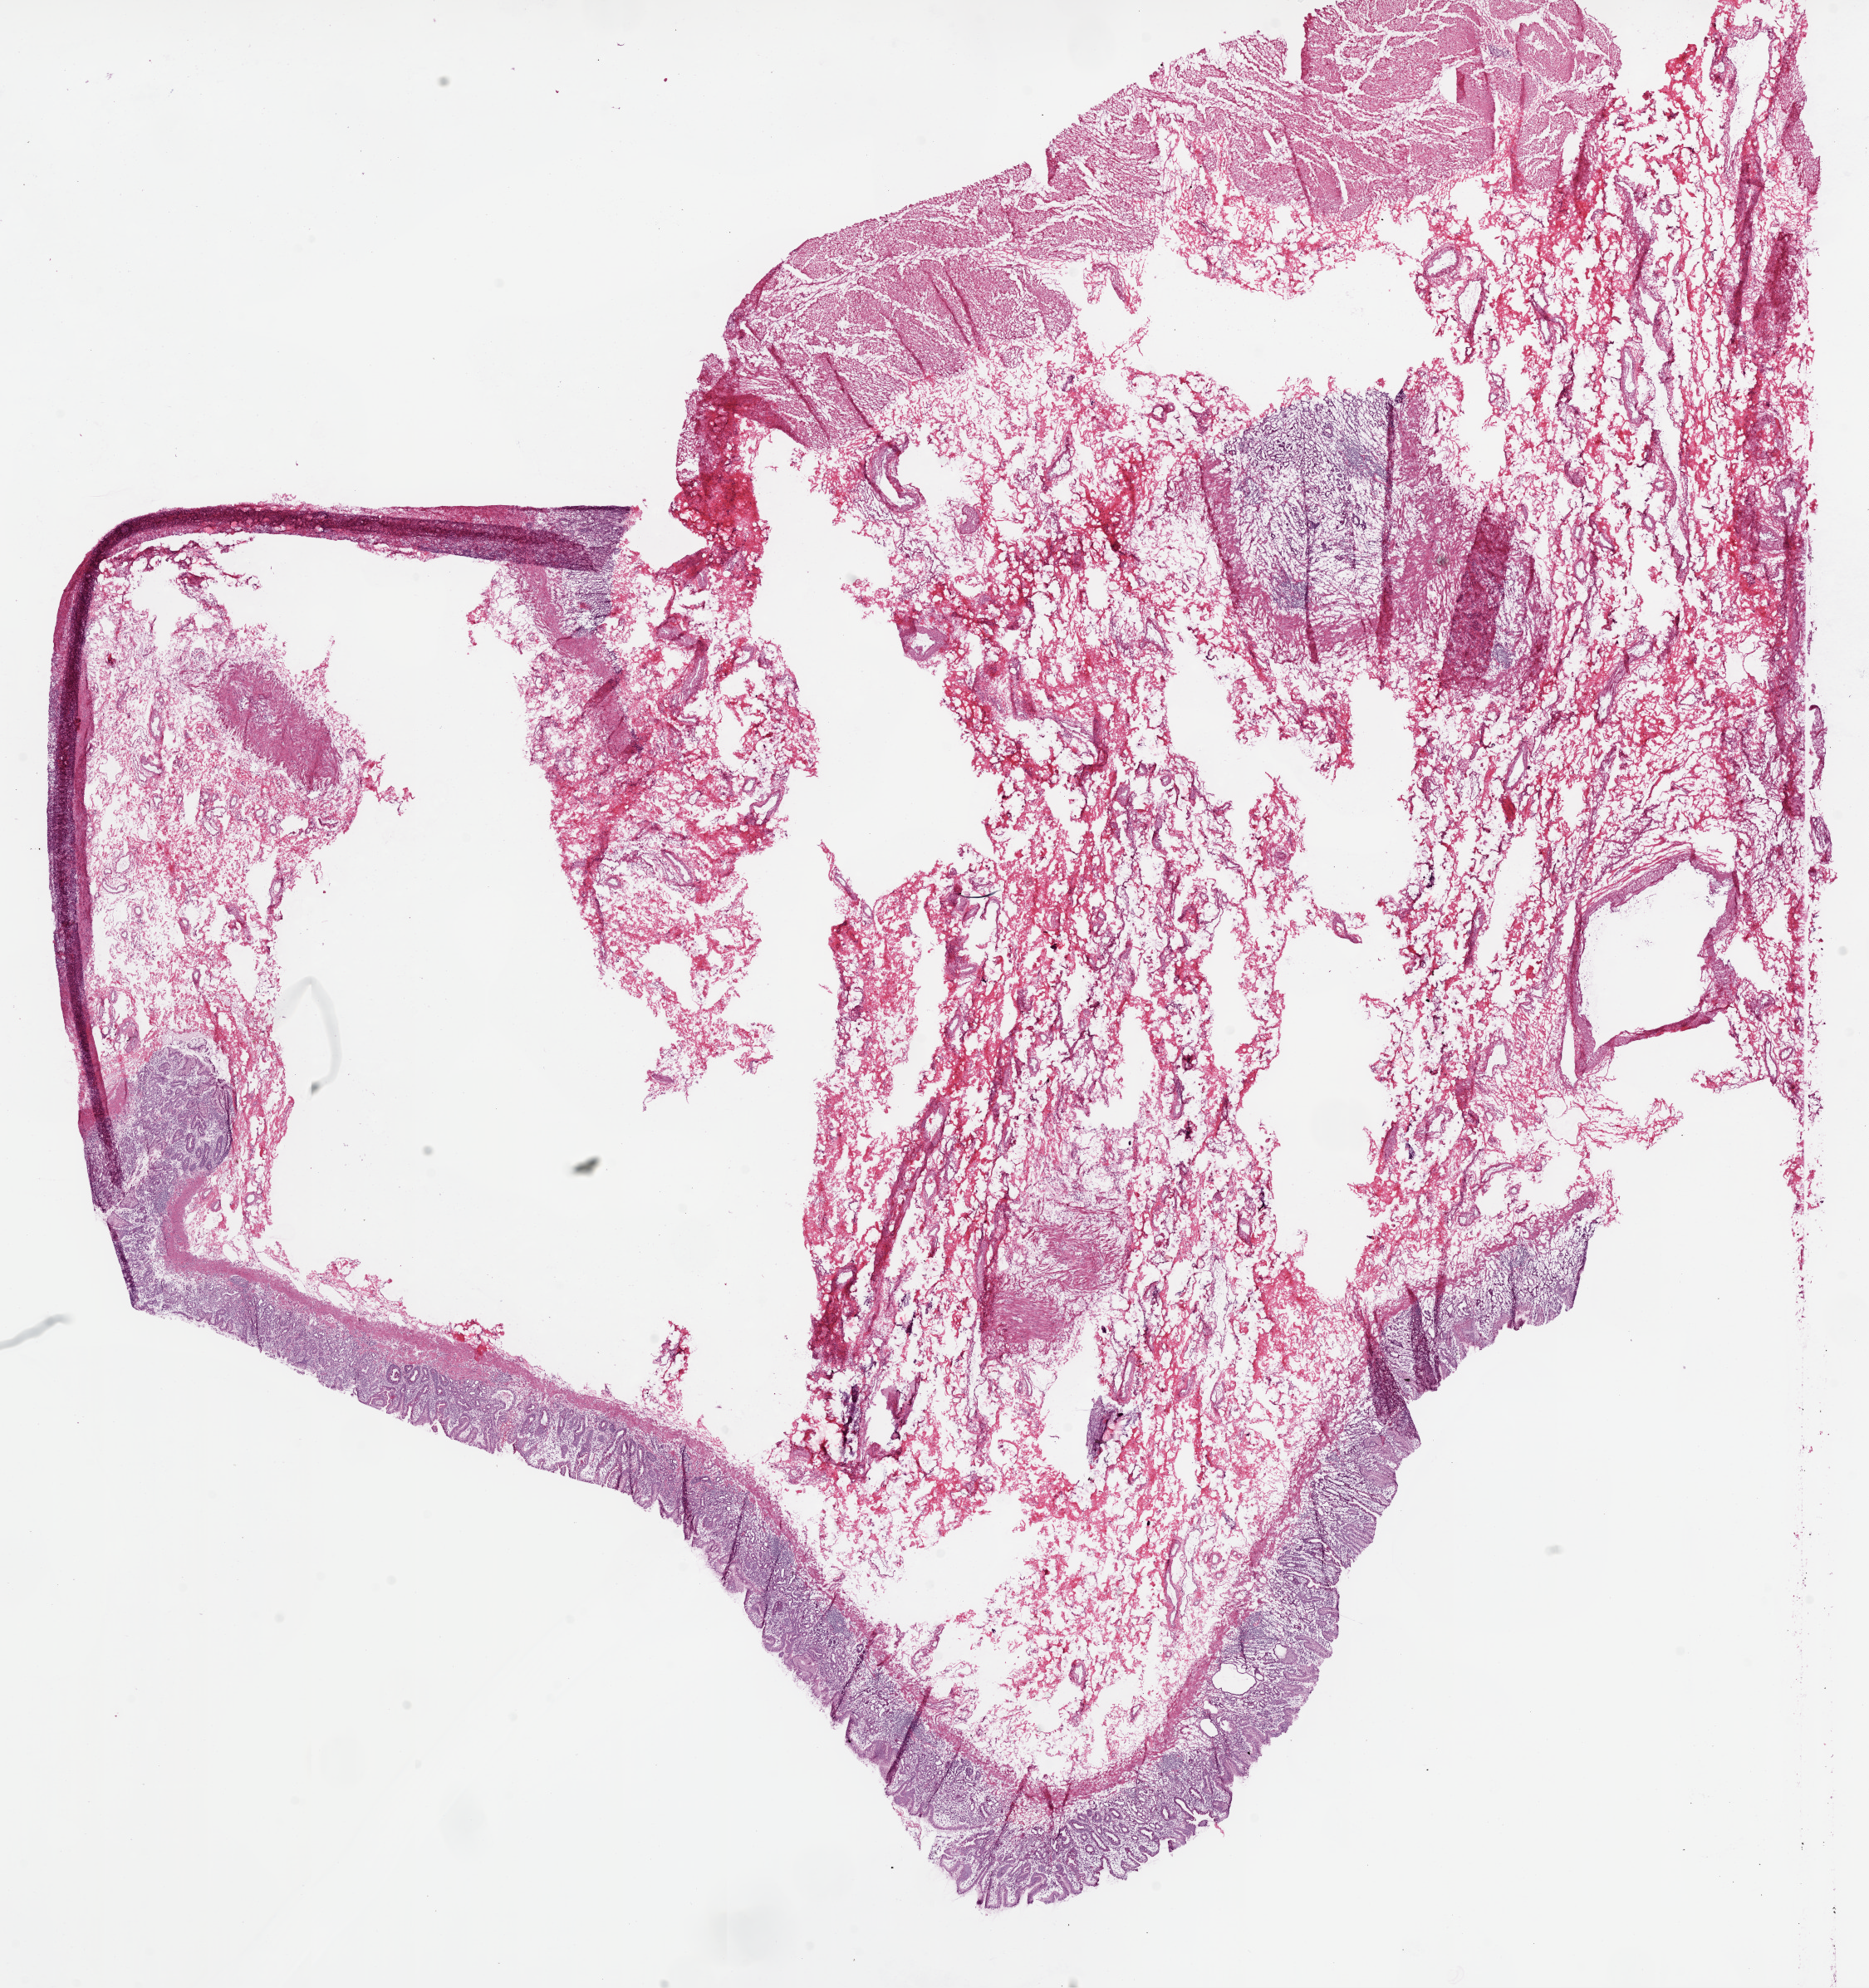
Digitized Hematoxylin and eosin (H&E) stained tissue section (whole slide) — whole scanned area (about 18.1 x 19.2 mm, acquisition: 20x scan) shown as a low-resolution overview. Frozen section from the bottom of the tissue portion. Sample: solid tissue normal (non-tumour tissue), stomach. Patient: female, age at initial diagnosis 73 years.
This section: solid tissue normal (non-tumour) sample from the same patient. Patient diagnosis: Adenocarcinoma, NOS.